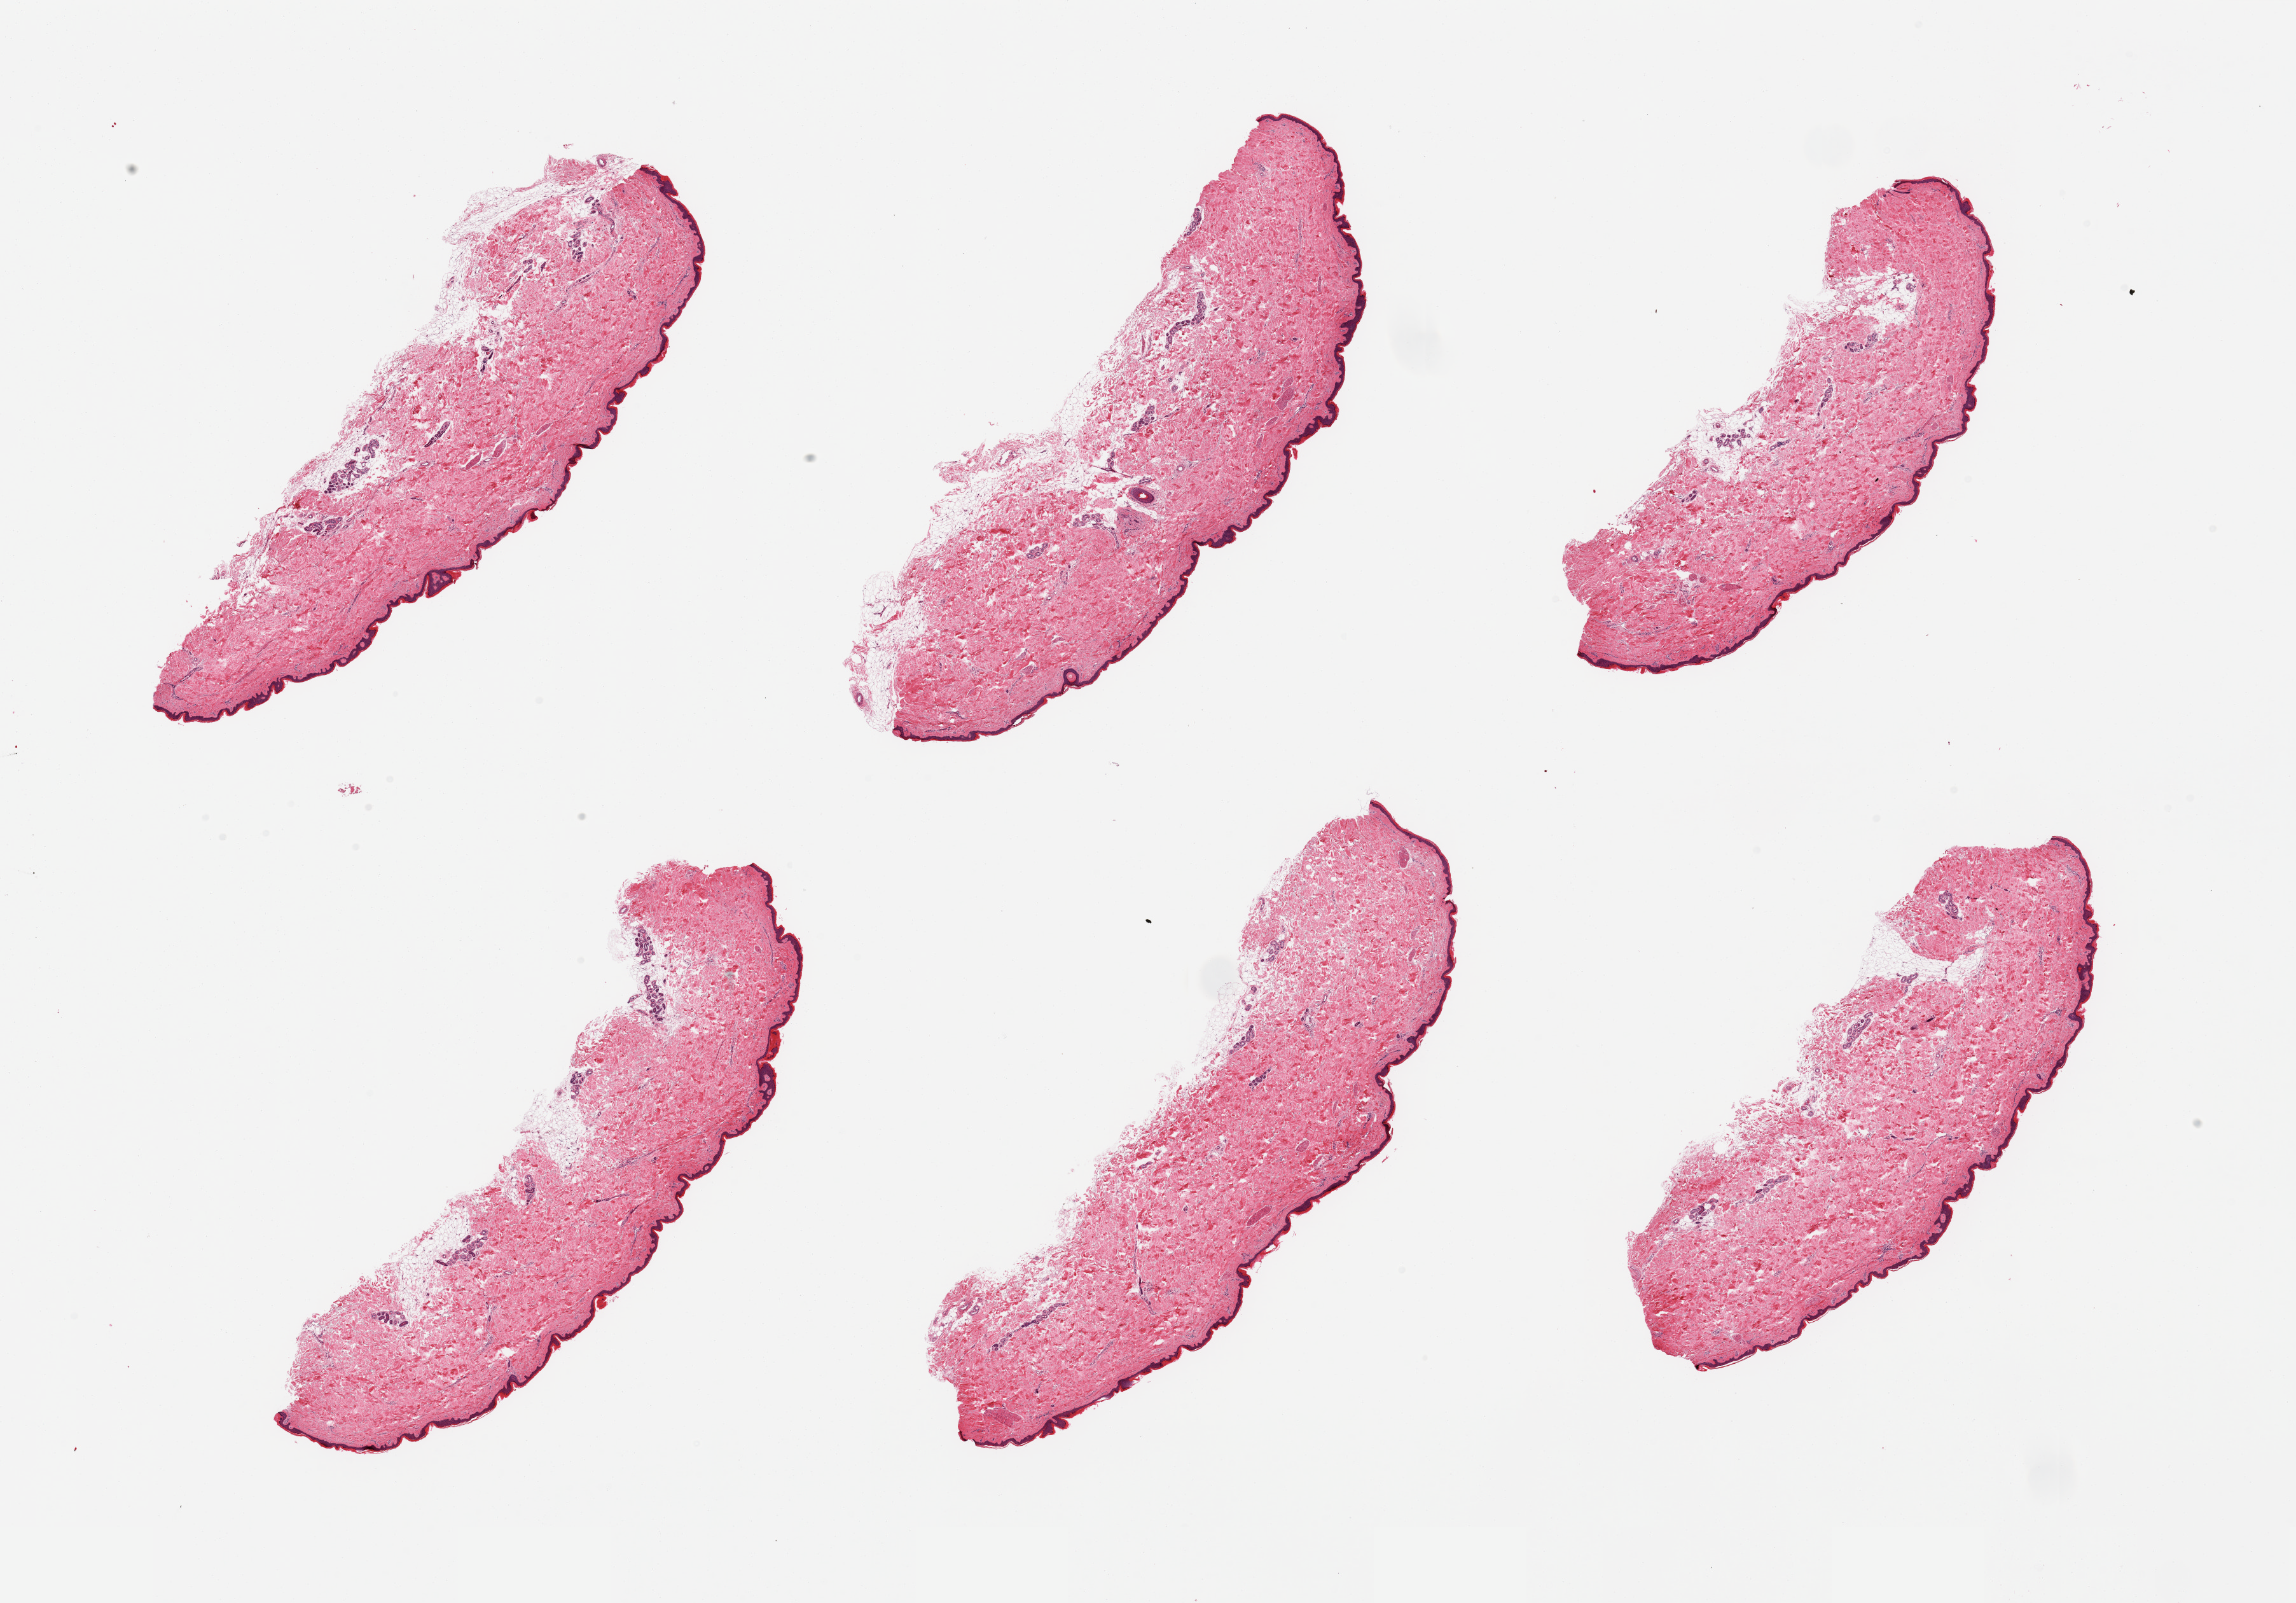
H&E whole-slide image — whole scanned area (about 28.5 x 19.9 mm) shown as a low-resolution overview, PAXgene-fixed paraffin-embedded (PFPE) section, sampled site (target tissue): skin of lower leg, donor tissue sample. Male donor.
Review note (as recorded): 6 pieces, minimal dermal fat; squamous epithelium is ~40 microns.